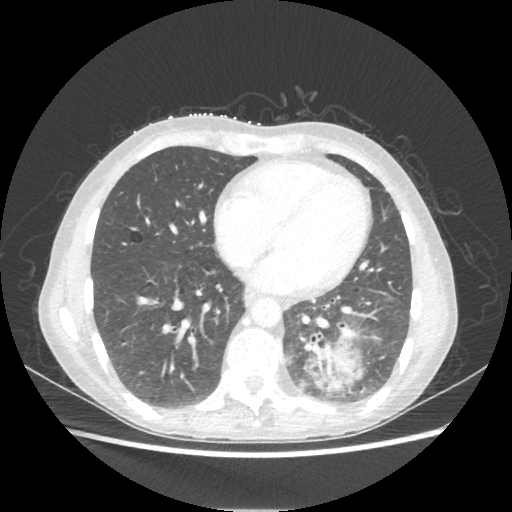
Chest CT, one axial slice. Slice 85 of 221 in the series (ordered by position). Lung window (W 1500 / L -600 HU). 1.25 mm slice thickness. 512 × 512 image matrix, field of view 360 × 360 mm. Patient: female, 53 years. From the clinical record (not read from this slice): clinical TNM (as recorded): T3 N0 M0.
Outlined on this slice (rectangle marked by the reading radiologist):
- lung tumour (recorded histology: adenocarcinoma): bounding box [x1, y1, x2, y2] px = [304, 339, 362, 392]